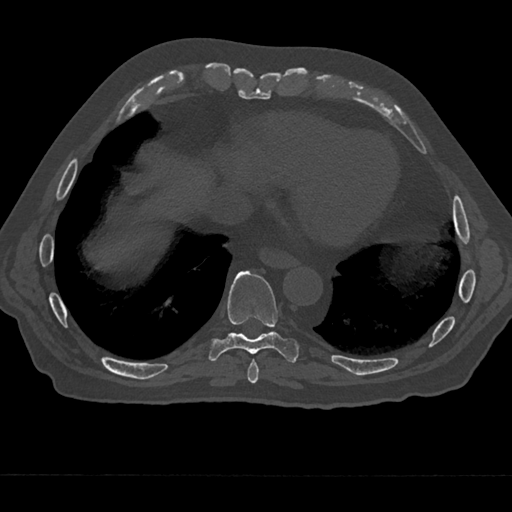
CT including the spine, one axial slice. Position 262 of 797 along the scan axis. Reconstruction kernel Br40s/3. 120 kVp. Bone window (W 1800 / L 400 HU). 0.5 mm slice thickness. 512 × 512 image matrix, field of view 377 × 377 mm. Male patient, age 75 years. From the clinical record (not read from this slice): primary cancer: renal.
Annotated regions visible in this slice (semi-automatic segmentation, software-assisted and operator-edited):
- T8 vertebra: bounding box <247,358,259,384> (left, top, right, bottom; pixels)
- T9 vertebra: <208,271,300,363>